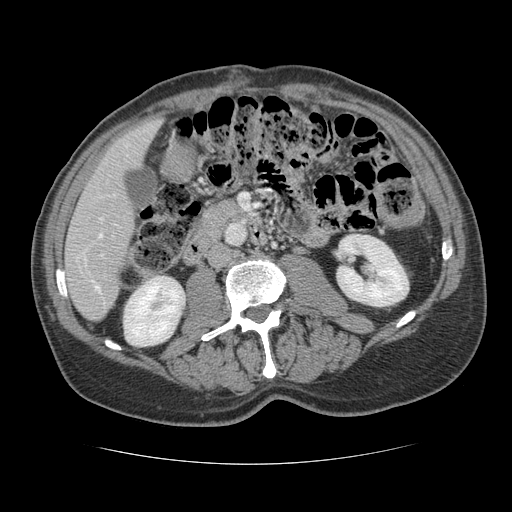
Contrast-enhanced abdominal CT, one axial slice. Slice 45 of 134 in the series (ordered by position). 120 kVp. Intravenous contrast given. Soft-tissue window (W 400 / L 40 HU). 512 × 512 image matrix, field of view 377 × 377 mm. Male patient, age 68 years. Case-level facts recorded for this patient, not image findings: diagnosis: colorectal cancer liver metastases, imaged before liver resection; multiple liver metastases: yes; largest metastasis: 2.2 cm; disease in both lobes: no.
Annotated regions visible in this slice (manually delineated by an expert):
- hepatic veins: bounding box (x1, y1, x2, y2) in pixels: (99, 218, 103, 237)
- liver: (65, 119, 160, 320)
- planned liver remnant (the part of the liver to remain after resection): (65, 119, 160, 320)
- portal vein (with intrahepatic branches): (95, 254, 103, 292)